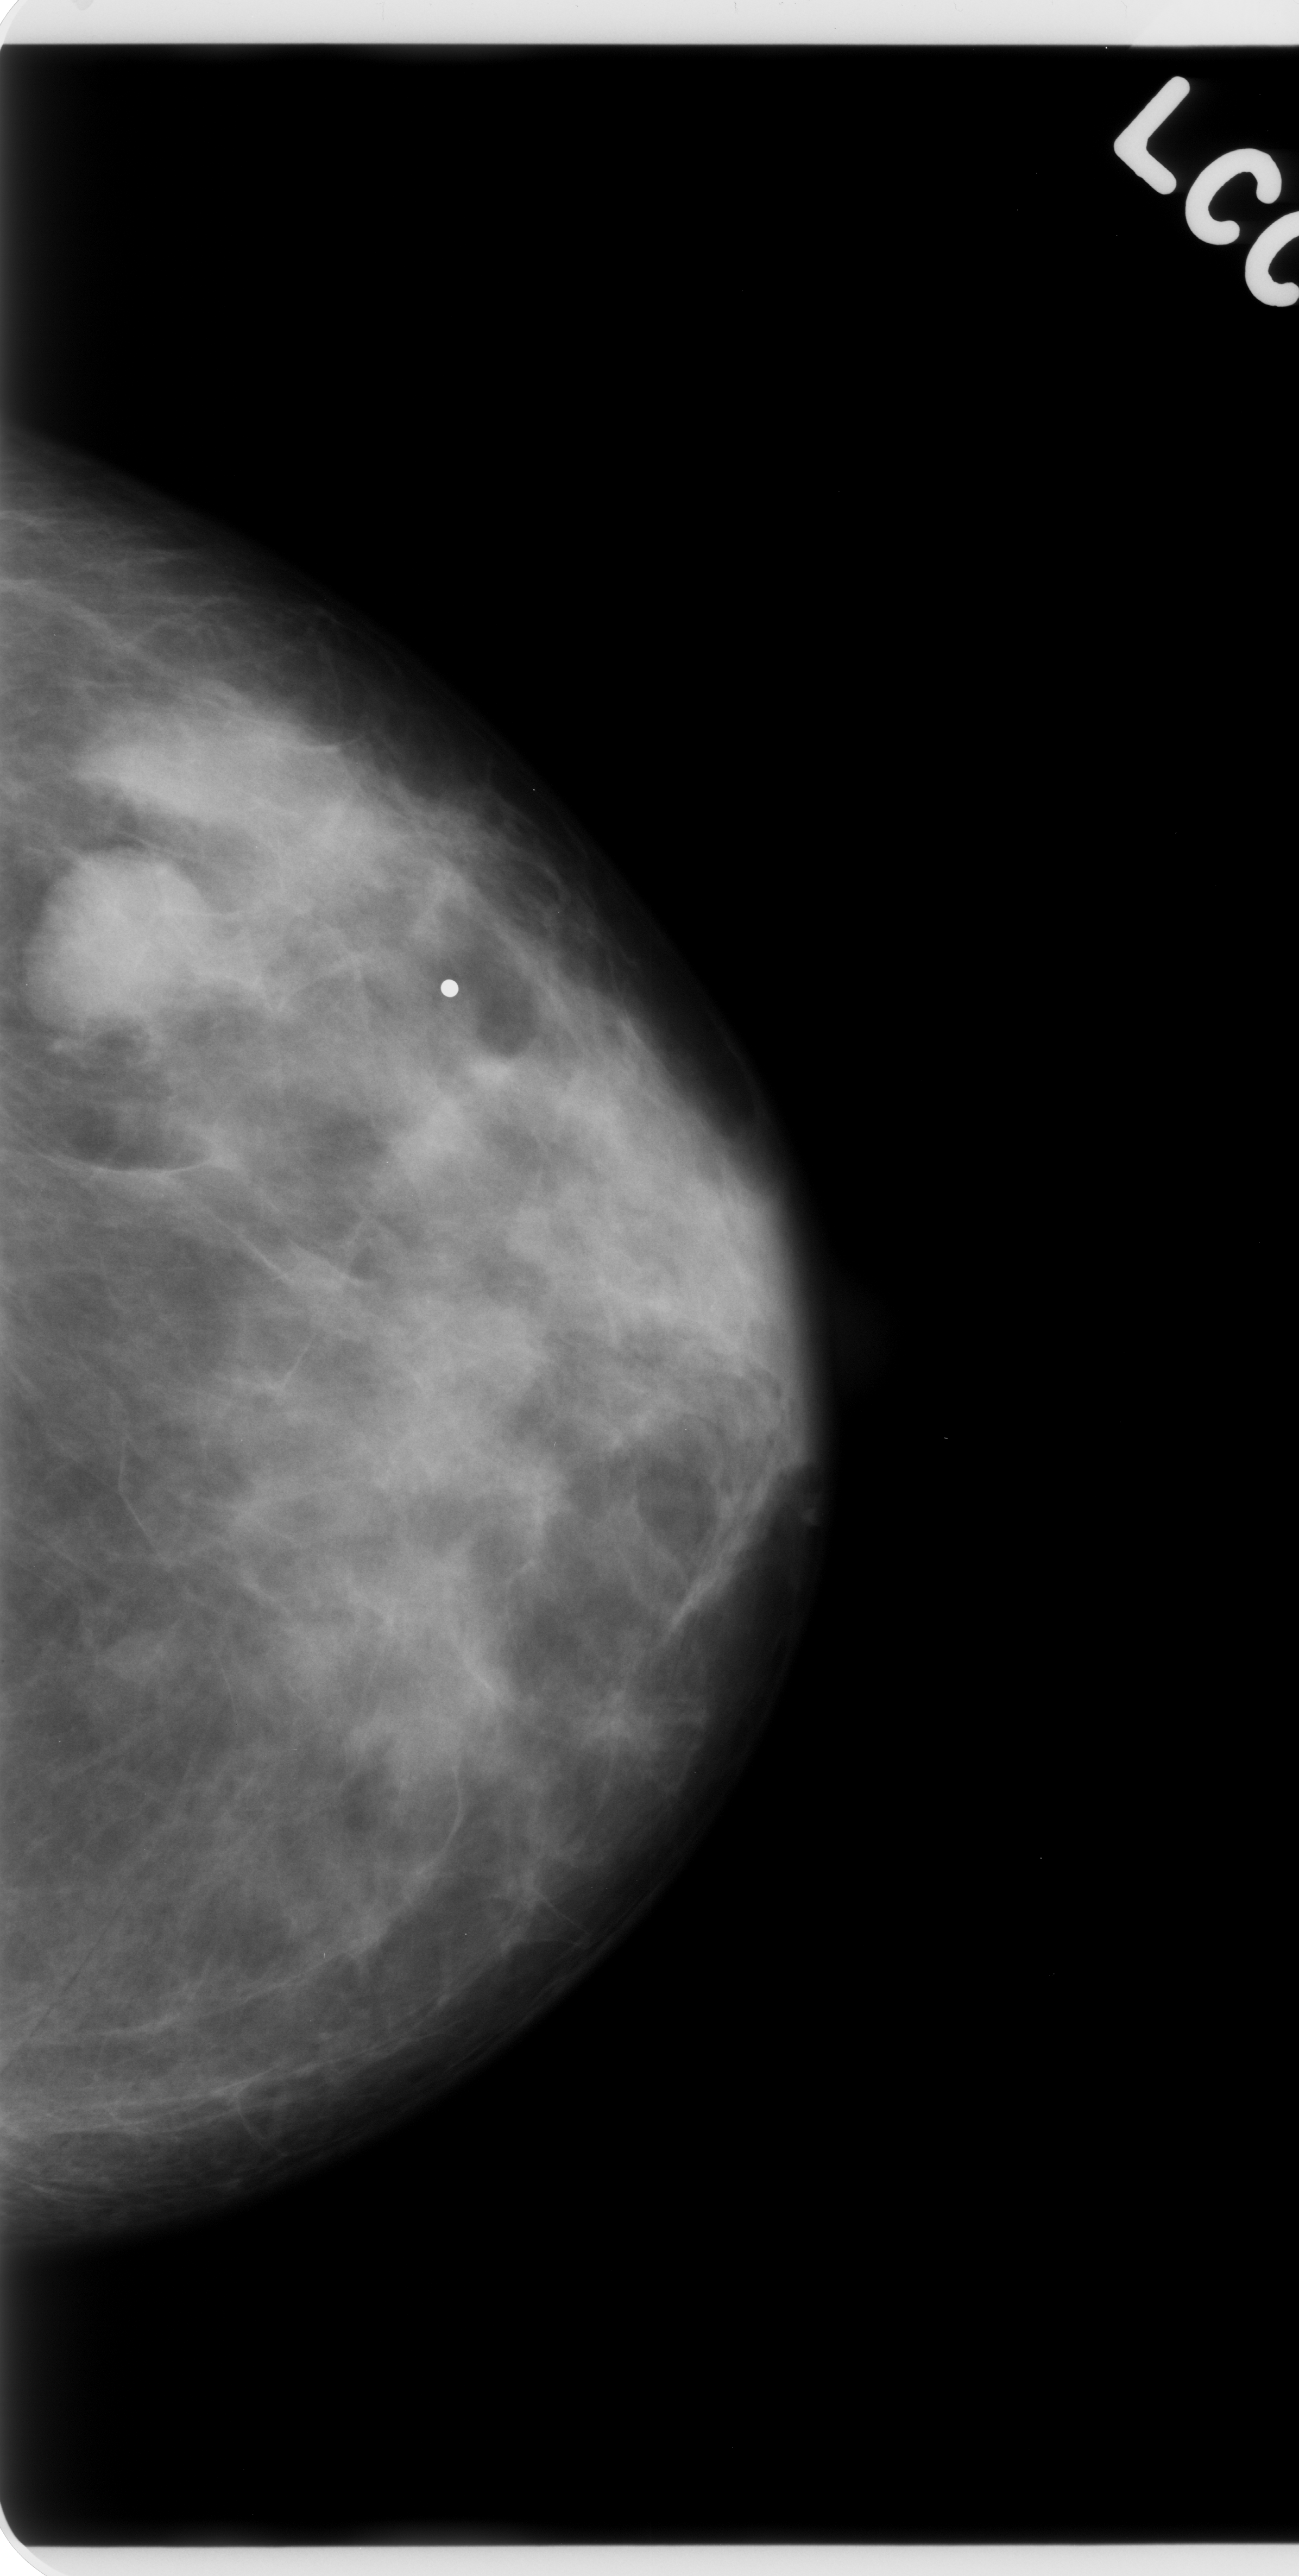
Mammogram (digitized film); left breast; craniocaudal (CC) view.
Mass, shape oval, margins circumscribed; BI-RADS assessment category 4; subtlety rating 5 on a 1 (subtle) to 5 (obvious) scale; pathology (as recorded): malignant.